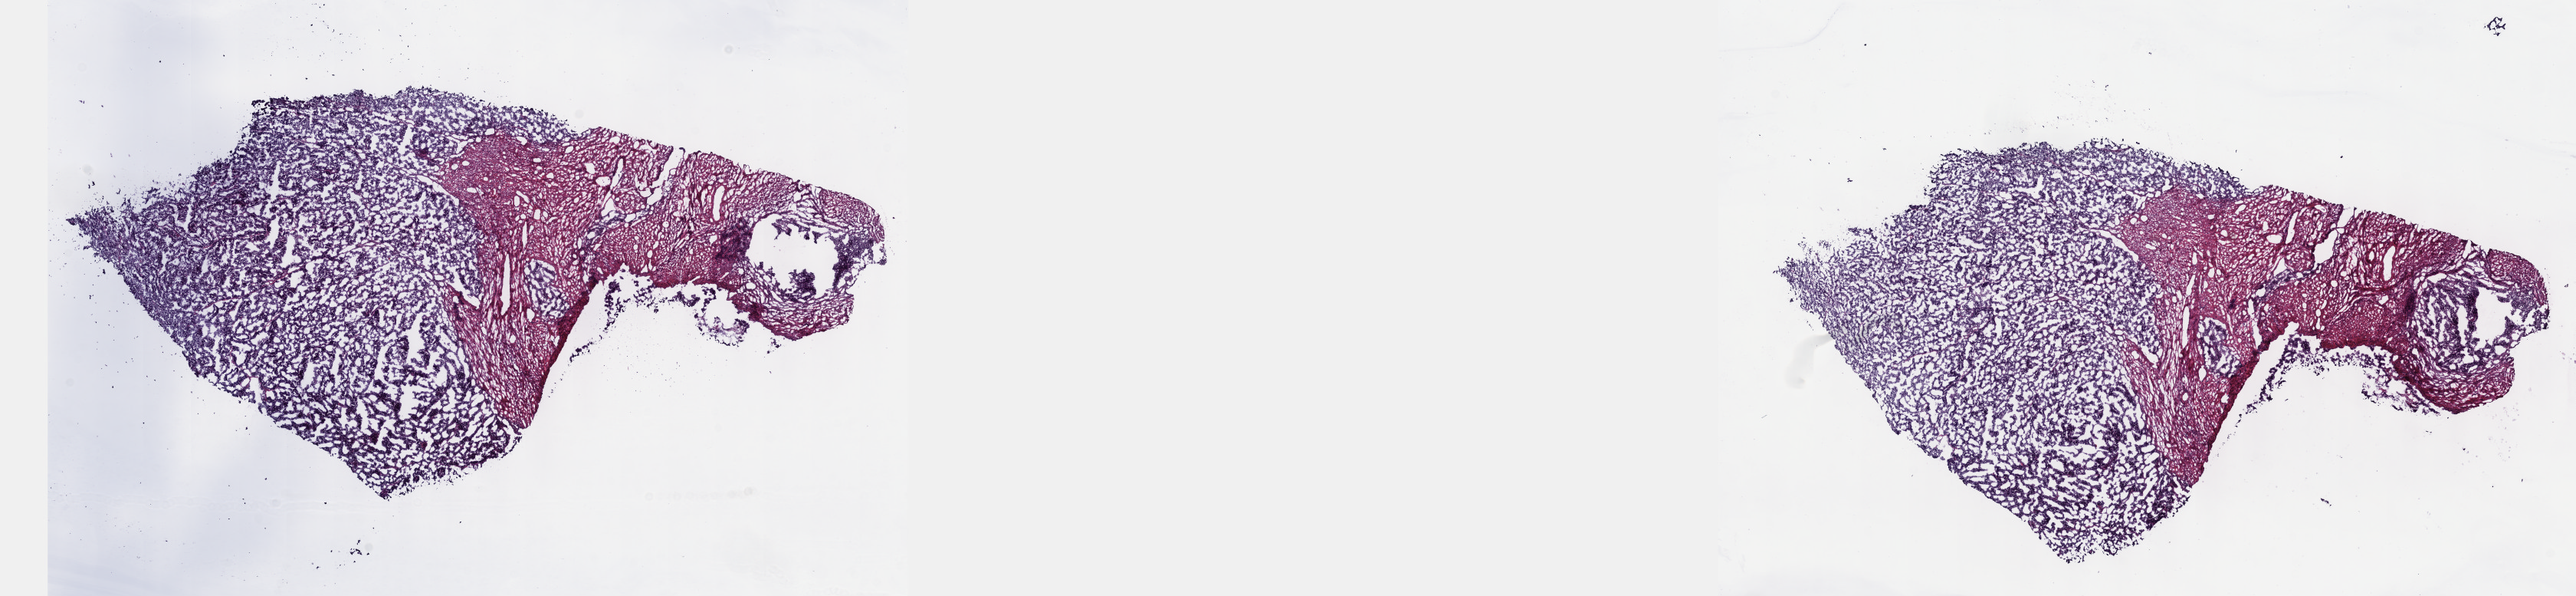
Whole-slide histology image, H&E-stained, a low-resolution overview of the entire scanned area, about 27.2 x 6.3 mm (from a 40x scan); frozen section from the top of the tissue portion; primary tumour sample from the uterus. Female, age 74 years at initial diagnosis. Histologic grade: G2 (moderately differentiated). Composition of this section per pathologist review: tumour cells 70%, tumour nuclei 80%, normal cells 20%, stromal cells 10%, necrosis 0%. Infiltration values recorded for this section: lymphocyte infiltration 0%, monocyte infiltration 0%, neutrophil infiltration 0%.
- pathologic diagnosis: Endometrioid adenocarcinoma, NOS (endometrium)
- FIGO stage: IA